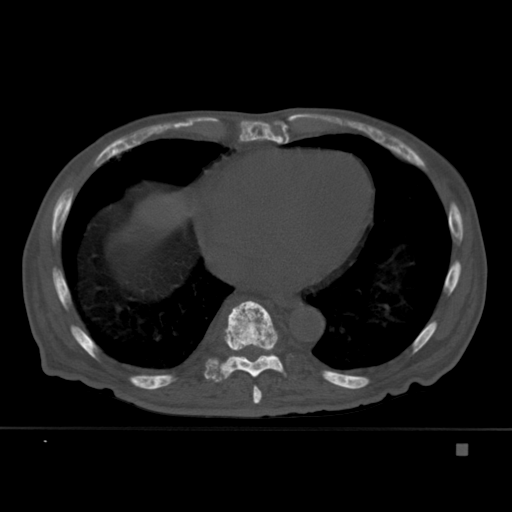
CT including the spine, one axial slice. Position 248 of 451 along the scan axis. Bone window (W 1800 / L 400 HU). 1.5 mm slice thickness. 512 × 512 image matrix, field of view 378 × 378 mm. Patient: male, 75 years. From the clinical record (not read from this slice): primary cancer: prostate.
Outlined on this slice (semi-automatically segmented with operator editing):
- T10 vertebra: bounding box (x1, y1, x2, y2) in pixels: (234, 353, 276, 357)
- T8 vertebra: (248, 372, 262, 404)
- T9 vertebra: (204, 300, 293, 382)